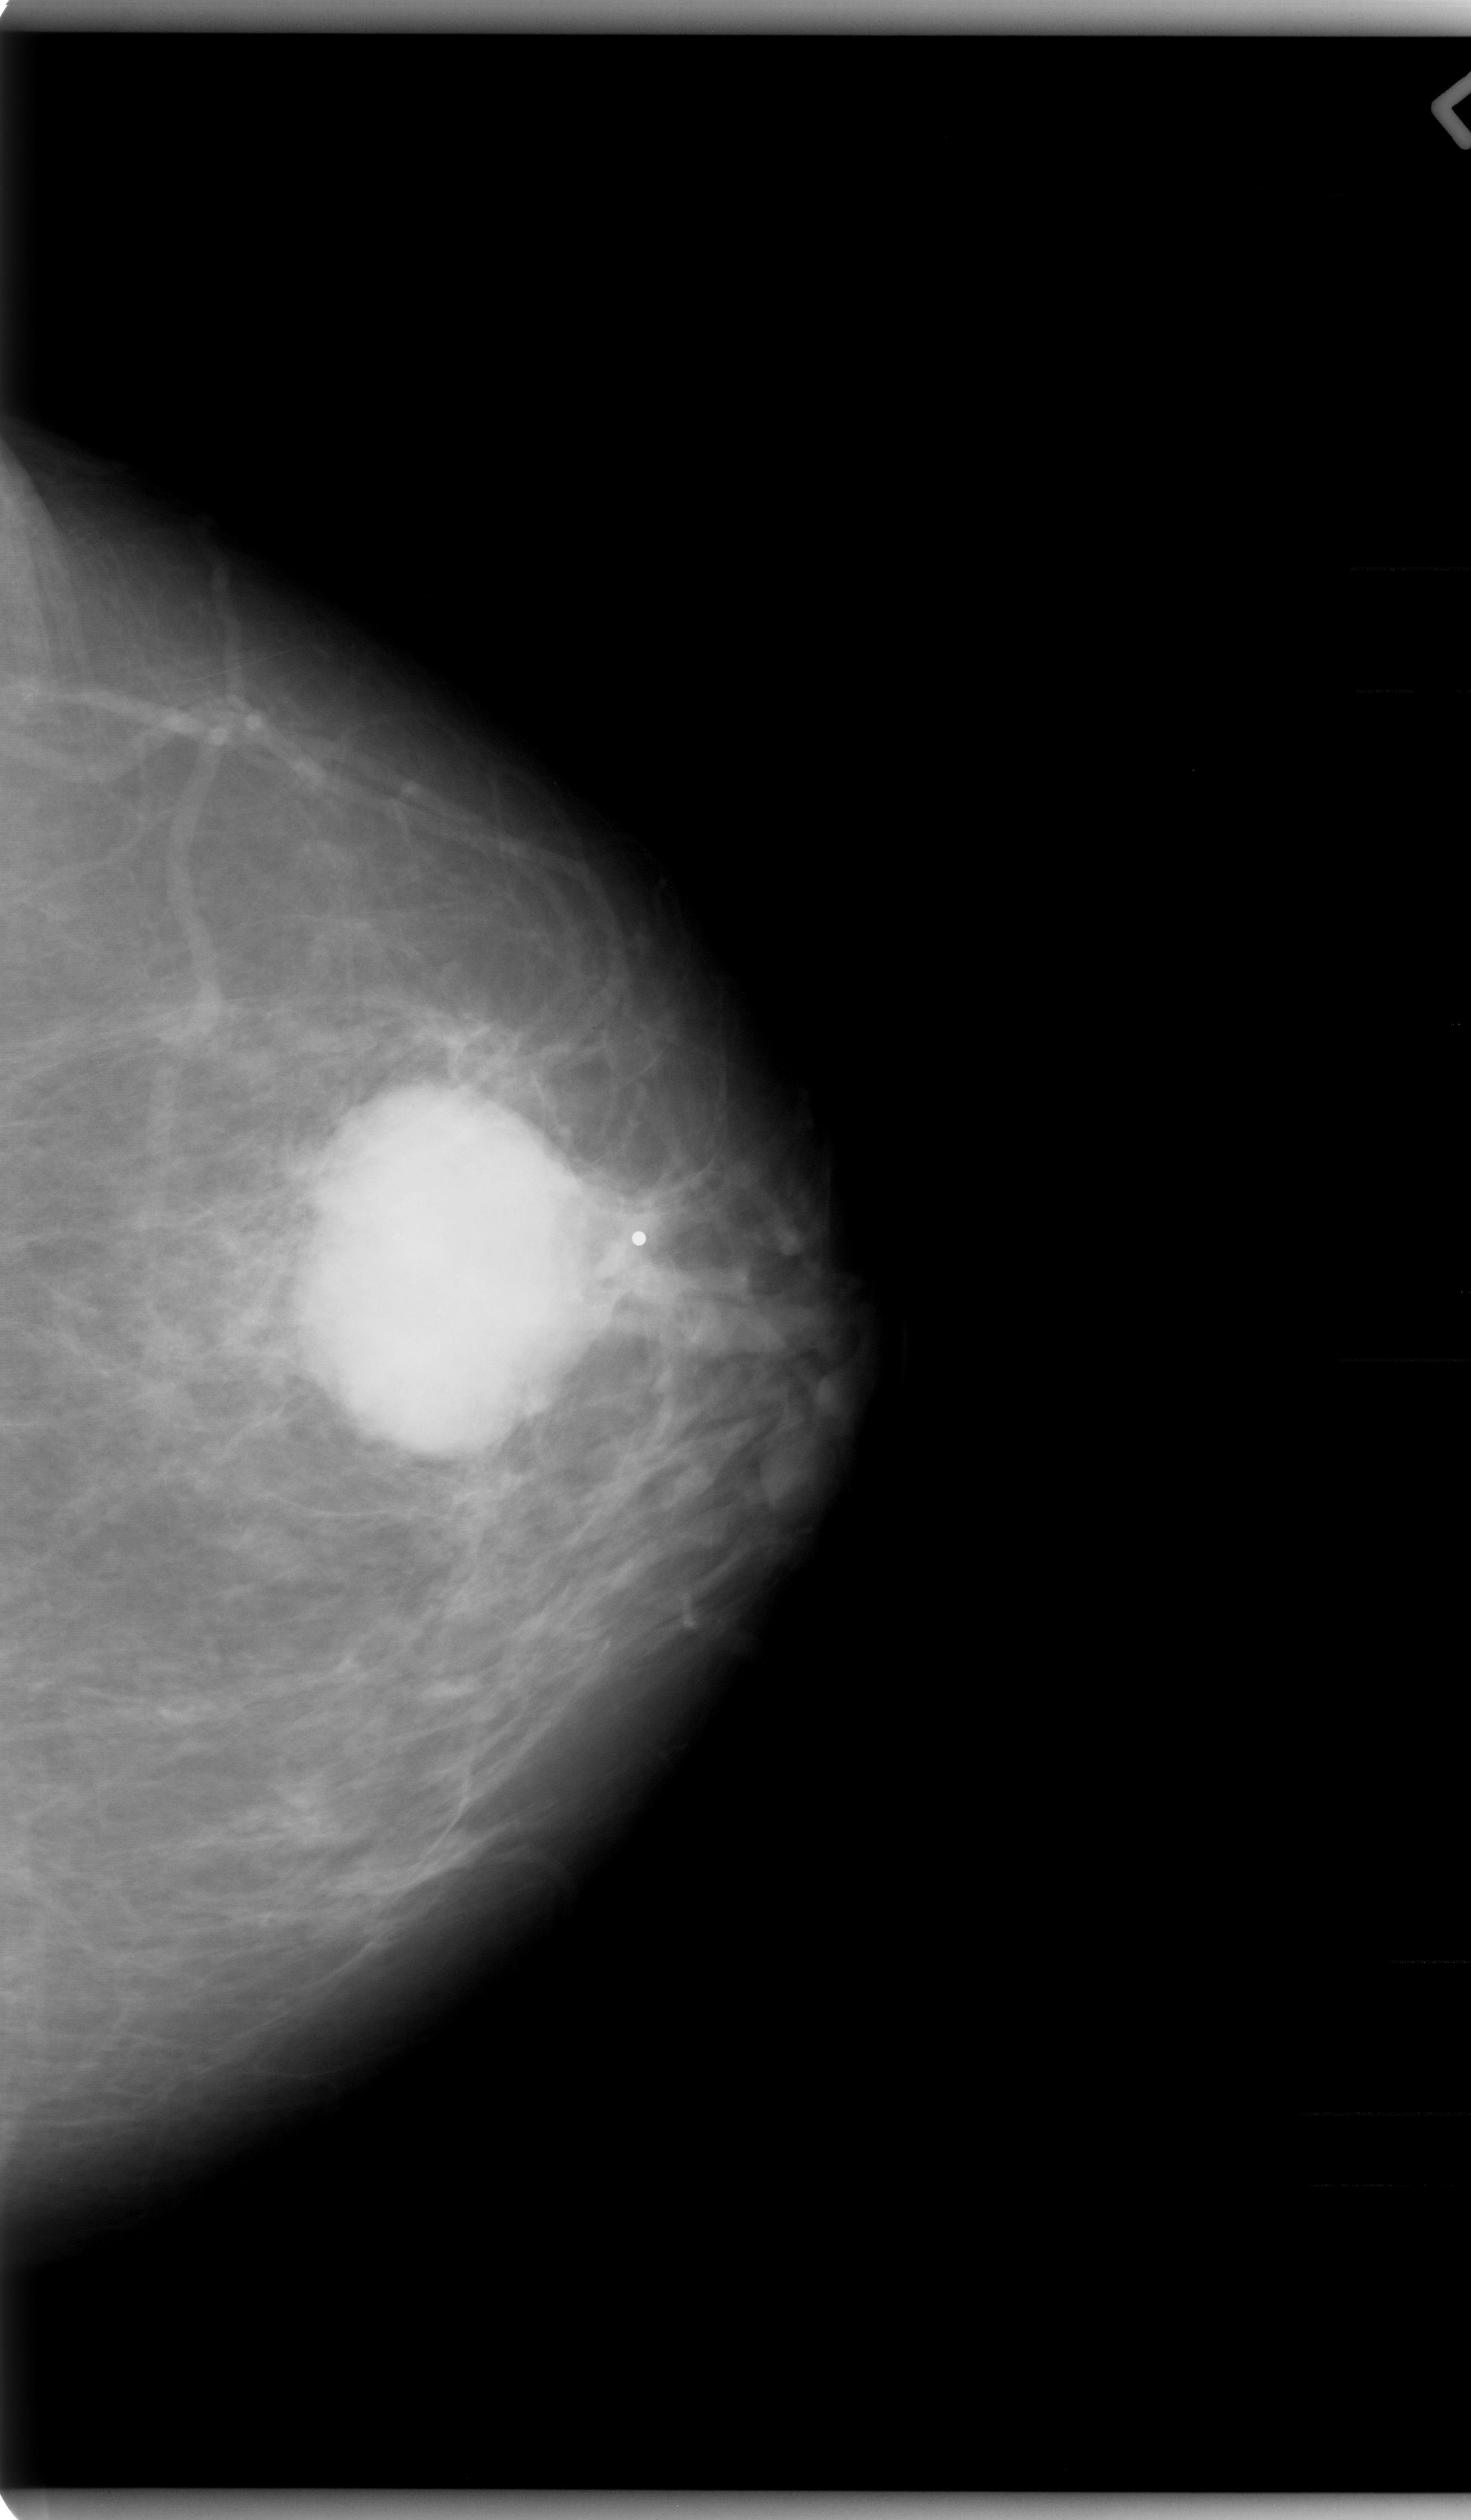
Scanned film-screen mammogram; left breast; CC view; 1471 × 2520 image matrix.
Expert-marked regions of interest on this image (one box per marked abnormality):
- mass, shape oval, margins microlobulated; BI-RADS assessment category 5; subtlety rating 5 on a 1 (subtle) to 5 (obvious) scale; pathology (as recorded): malignant: bounding box [x1, y1, x2, y2] px = [287, 1093, 606, 1416]